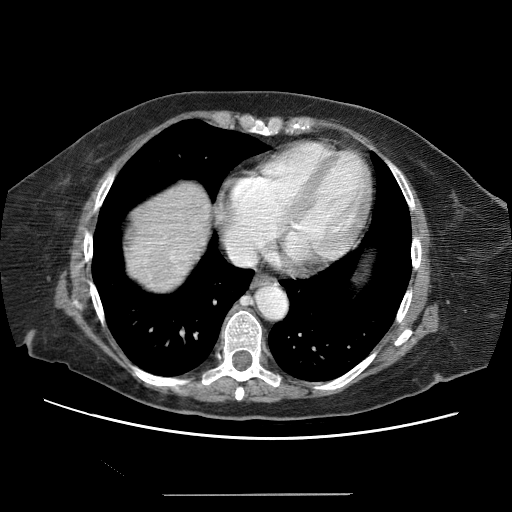
Contrast-enhanced abdominal CT (liver protocol), one axial slice. Position 60 of 65 along the scan axis. 120 kVp. Soft-tissue window (W 400 / L 40 HU). 2.5 mm slice thickness. 512 × 512 image matrix, field of view 380 × 380 mm. From the clinical record (not read from this slice): diagnosis: hepatocellular carcinoma (patient treated with transarterial chemoembolisation; whether this scan precedes or follows treatment is not stated here); TNM stage (as recorded): Stage-IIIB; Child-Pugh class: A; tumour differentiation: moderately differentiated; tumour nodularity: uninodular.
Annotated regions visible in this slice (semi-automatic segmentation, software-assisted and operator-edited):
- abdominal aorta: bounding box (x1, y1, x2, y2) in pixels: (258, 287, 287, 320)
- liver parenchyma outside the tumour (the mass and vessels are separate outlines, so this box may not span the whole liver): (134, 186, 206, 276)
- mass: (135, 237, 178, 285)
- liver vessels: (169, 222, 189, 273)